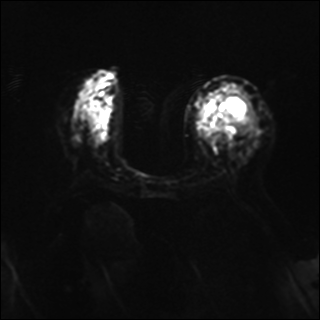
Breast MRI, one axial slice. Position 14 of 37 along the scan axis. Diffusion-weighted series; image 2 of 4 stored at this slice position (different b-values; order by instance number). 1.5 T. 4 mm slice thickness. 320 × 320 image matrix, field of view 320 × 320 mm. Female patient.
Structures marked on this image (expert manual segmentation):
- tumour on diffusion-weighted imaging: bounding box [x1, y1, x2, y2] px = [221, 97, 250, 132]